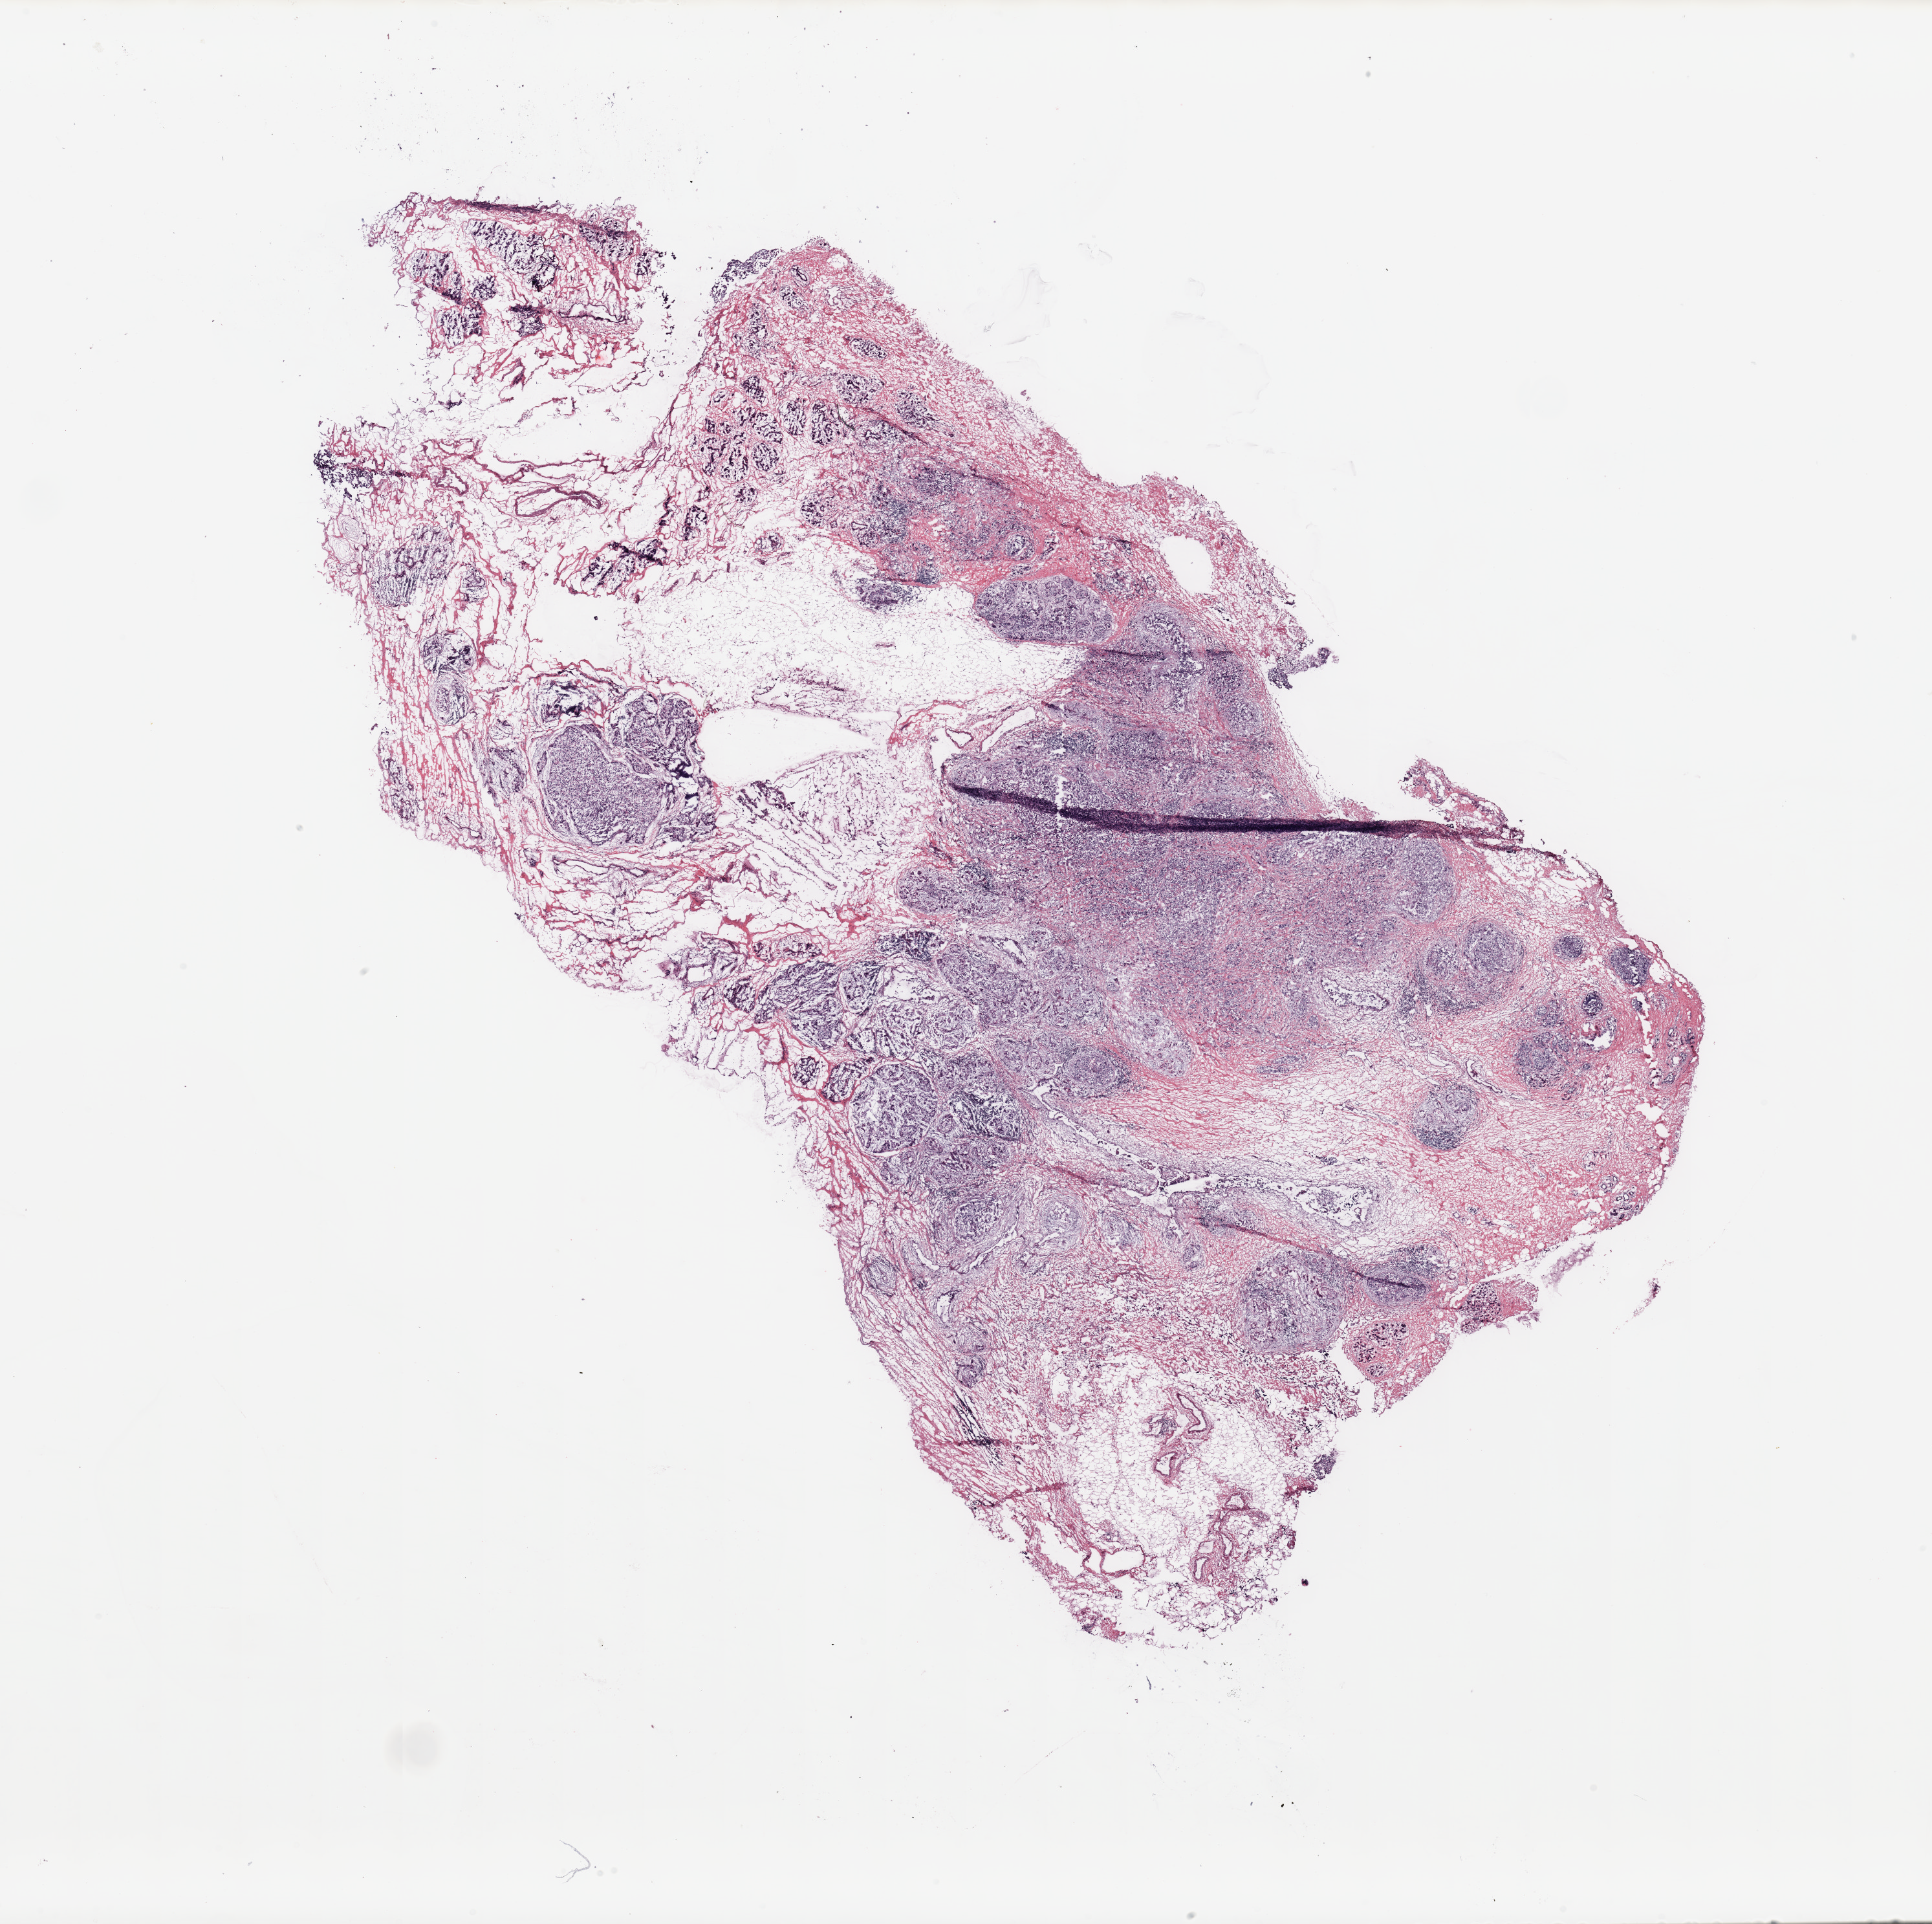
H&E whole-slide image, whole scanned area (about 23.6 x 23.5 mm, acquisition: 20x scan) shown as a low-resolution overview. Breast, tissue type not recorded.
• patient diagnosis (cohort enrolment): breast cancer (breast)